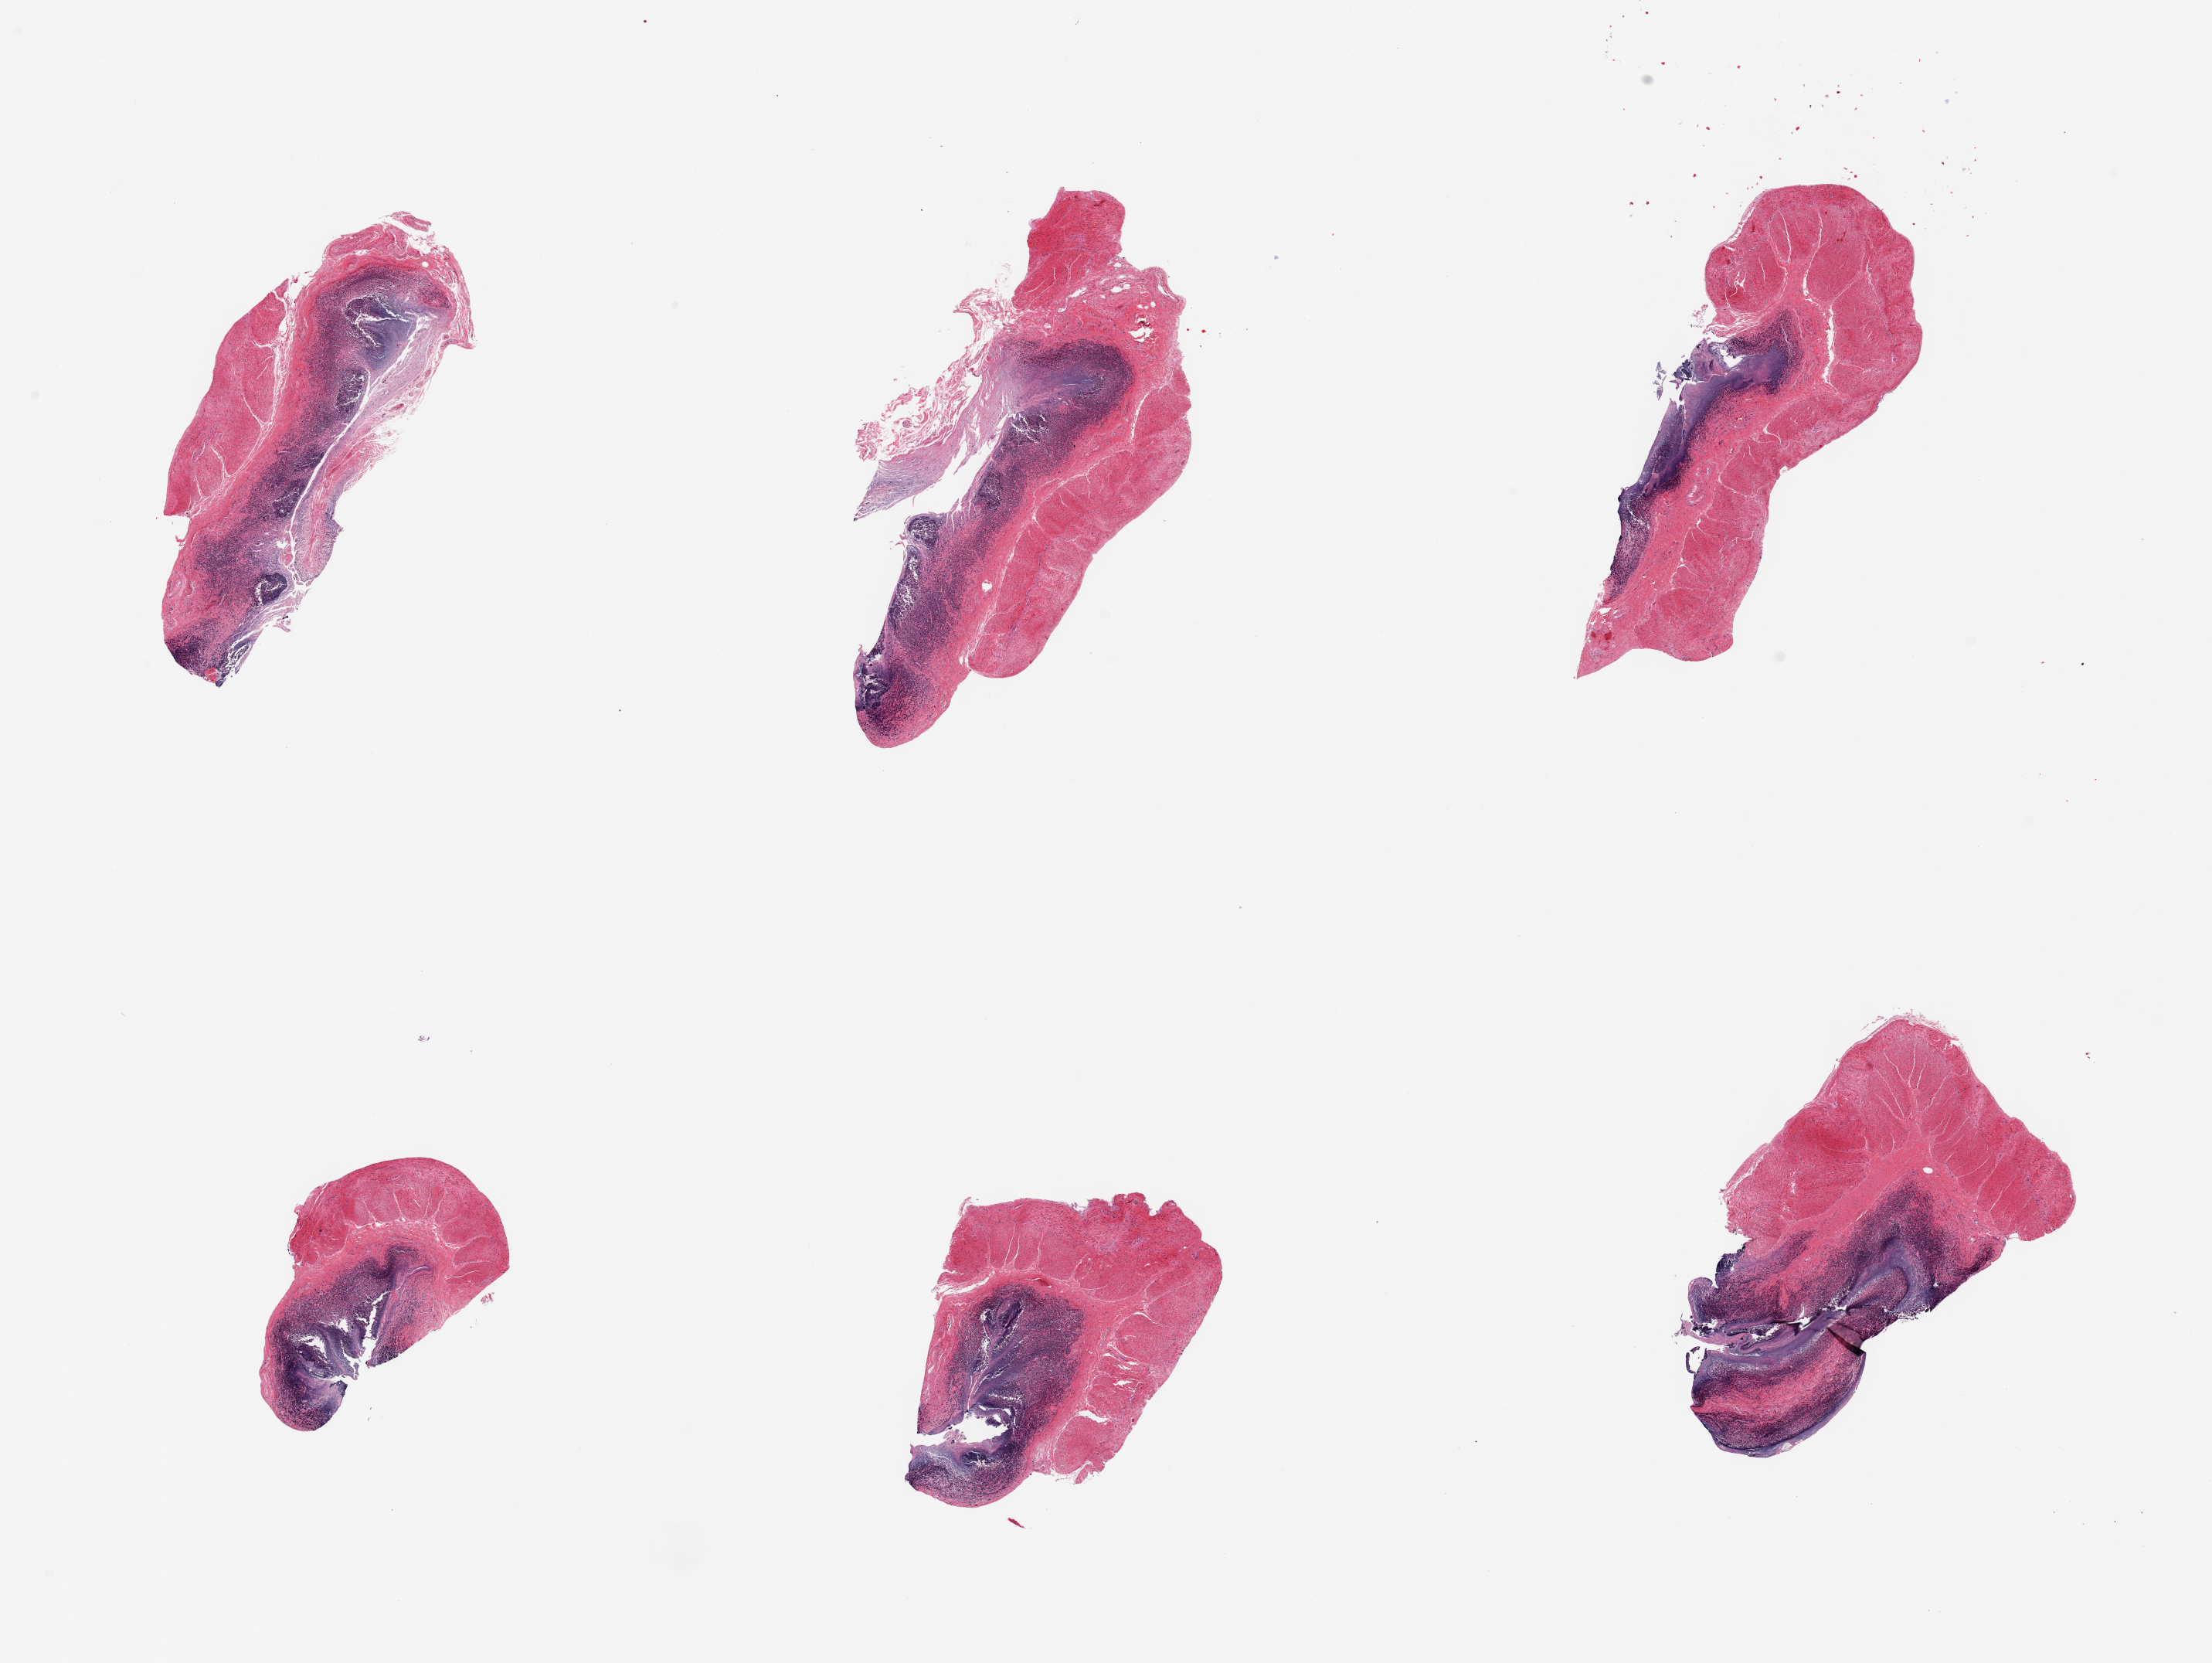
Whole-slide image, H&E stain, brightfield, low-resolution overview of the scanned area, about 22.6 x 17.0 mm. Donor sex: female.
• specimen: PAXgene-fixed paraffin-embedded (PFPE) section; section of gastroesophageal junction (target tissue); tissue donor sample